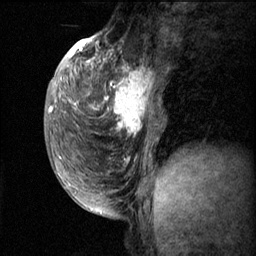
Breast MRI (dynamic contrast-enhanced), one sagittal slice; slice 22 of 60 in the series (ordered by position); dynamic contrast-enhanced series, image 2 of 3 at this slice position (ordered by acquisition); 1.5 T; TE 4.2 ms, TR 11.1 ms; 256 × 256 image matrix. Patient: female, 50 years.
Annotated regions visible in this slice (semi-automatic segmentation, software-assisted and operator-edited):
- analysis volume of interest (the breast-tissue region the enhancement analysis was run in; not a lesion): box from (x=82, y=56) to (x=168, y=143) px
- tumour enhancement mask (voxels above the 70 % enhancement threshold inside the analysis volume of interest): (x=82, y=58)–(x=154, y=137)